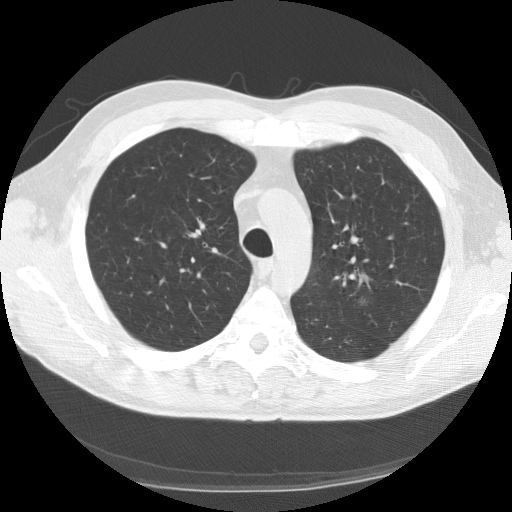
Low-dose screening chest CT, axial slice. Second screening round (one year after baseline). Lung window (W 1500 / L -600 HU). Standard (soft-tissue) reconstruction kernel (STANDARD). 120 kVp. Slice 37 of 152 in the series. 512 × 512 image matrix, field of view 370 × 370 mm. Male participant, aged 57 years at enrolment. Current smoker at enrolment.
- Lesion marked by an expert reader, box from (x=339, y=287) to (x=381, y=321) px.
- The exam's reader record, not a measurement of the box and not confirmed to be the same lesion: non-calcified nodule or mass ≥4 mm, left upper lobe, 12 × 7 mm, spiculated (stellate) margins, mixed attenuation, pre-existing on the prior screen: no.
- Later outcome: lung cancer diagnosed 419 days after this screen (after the third annual screen) — adenosquamous carcinoma, left upper lobe, poorly differentiated (G3), stage IA (AJCC 6th edition), 15 mm at pathology.